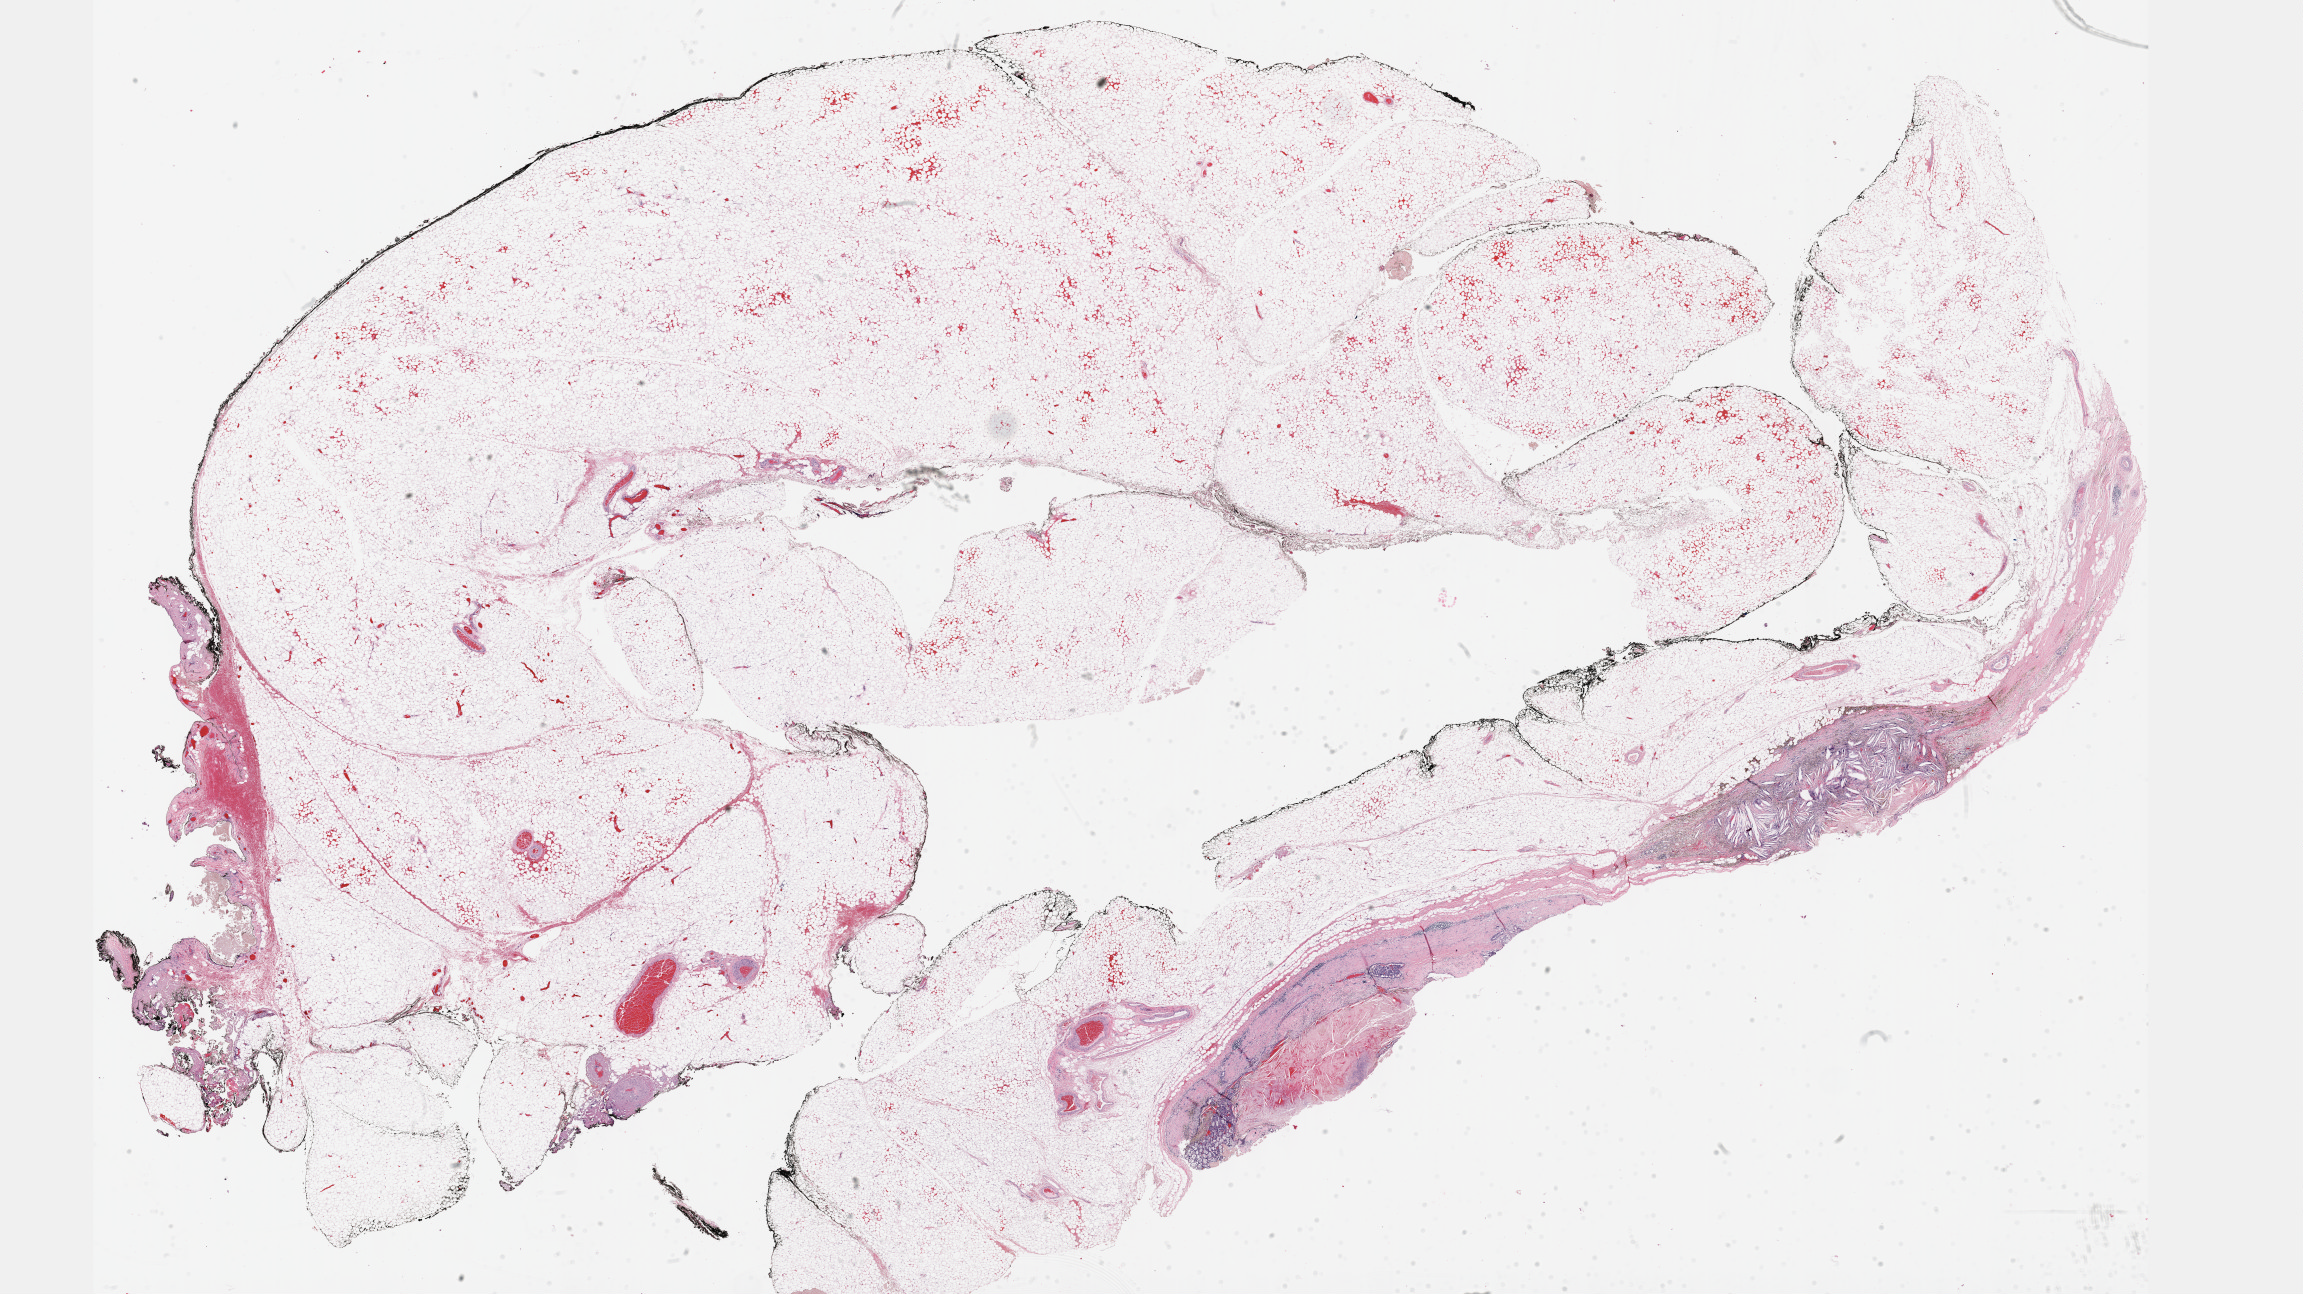
Hematoxylin and eosin (H&E) stained whole-slide image, whole scanned area (about 37.2 x 20.9 mm, slide scanned at 40x) shown as a low-resolution overview. Formalin-fixed paraffin-embedded (FFPE) diagnostic section. Kidney, primary tumour sample. Patient: male, age at initial diagnosis 85 years.
• pathologic diagnosis: Papillary adenocarcinoma, NOS
• AJCC pathologic stage: I
• TNM: T1b NX M0